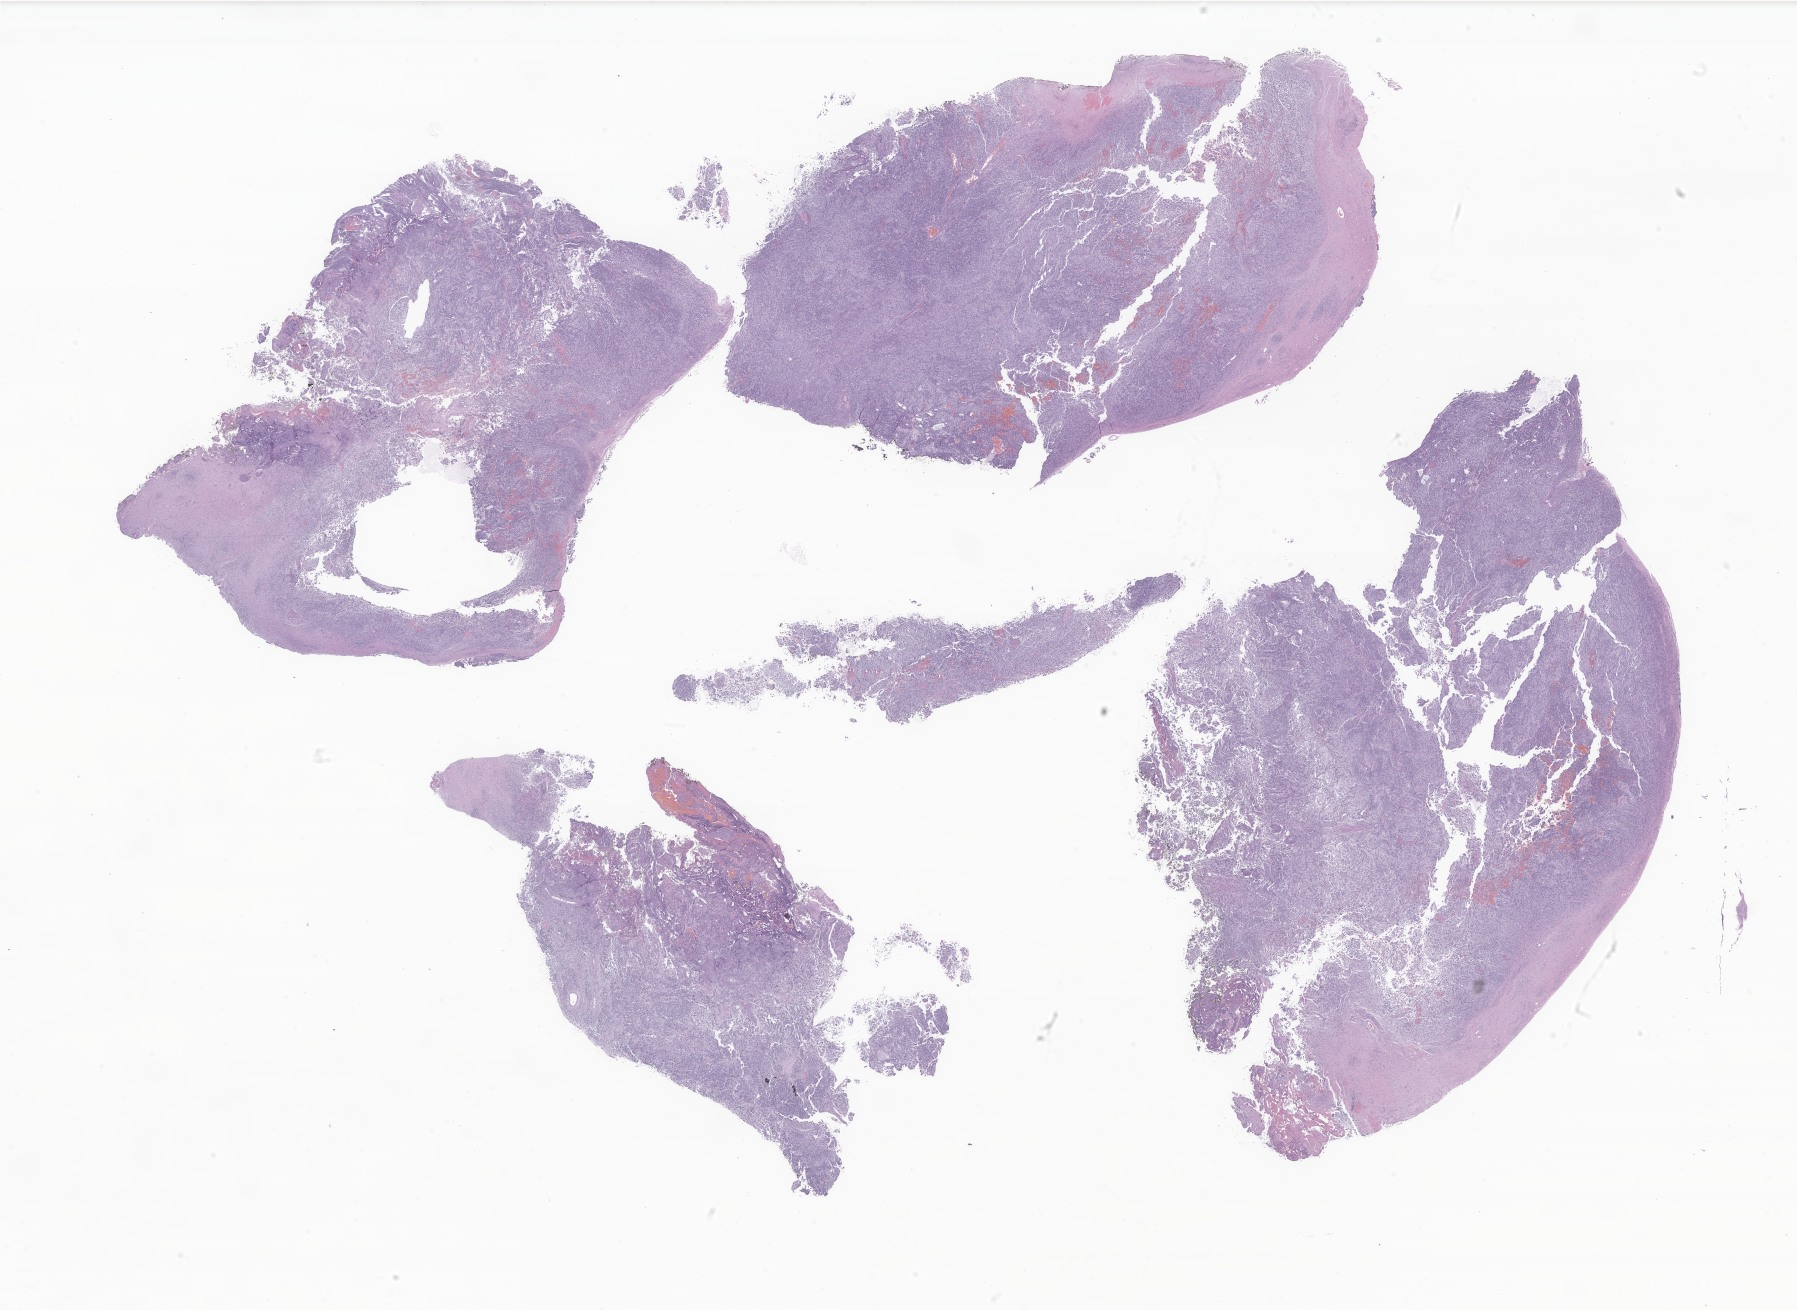
Digitized H&E-stained section of tumor tissue from the cerebellum — whole scanned area (about 30.3 x 22.1 mm) shown as a low-resolution overview. FFPE section. Patient: male, age 76 months (6 years 4 months).
Recorded diagnosis: Medulloblastoma, NOS.